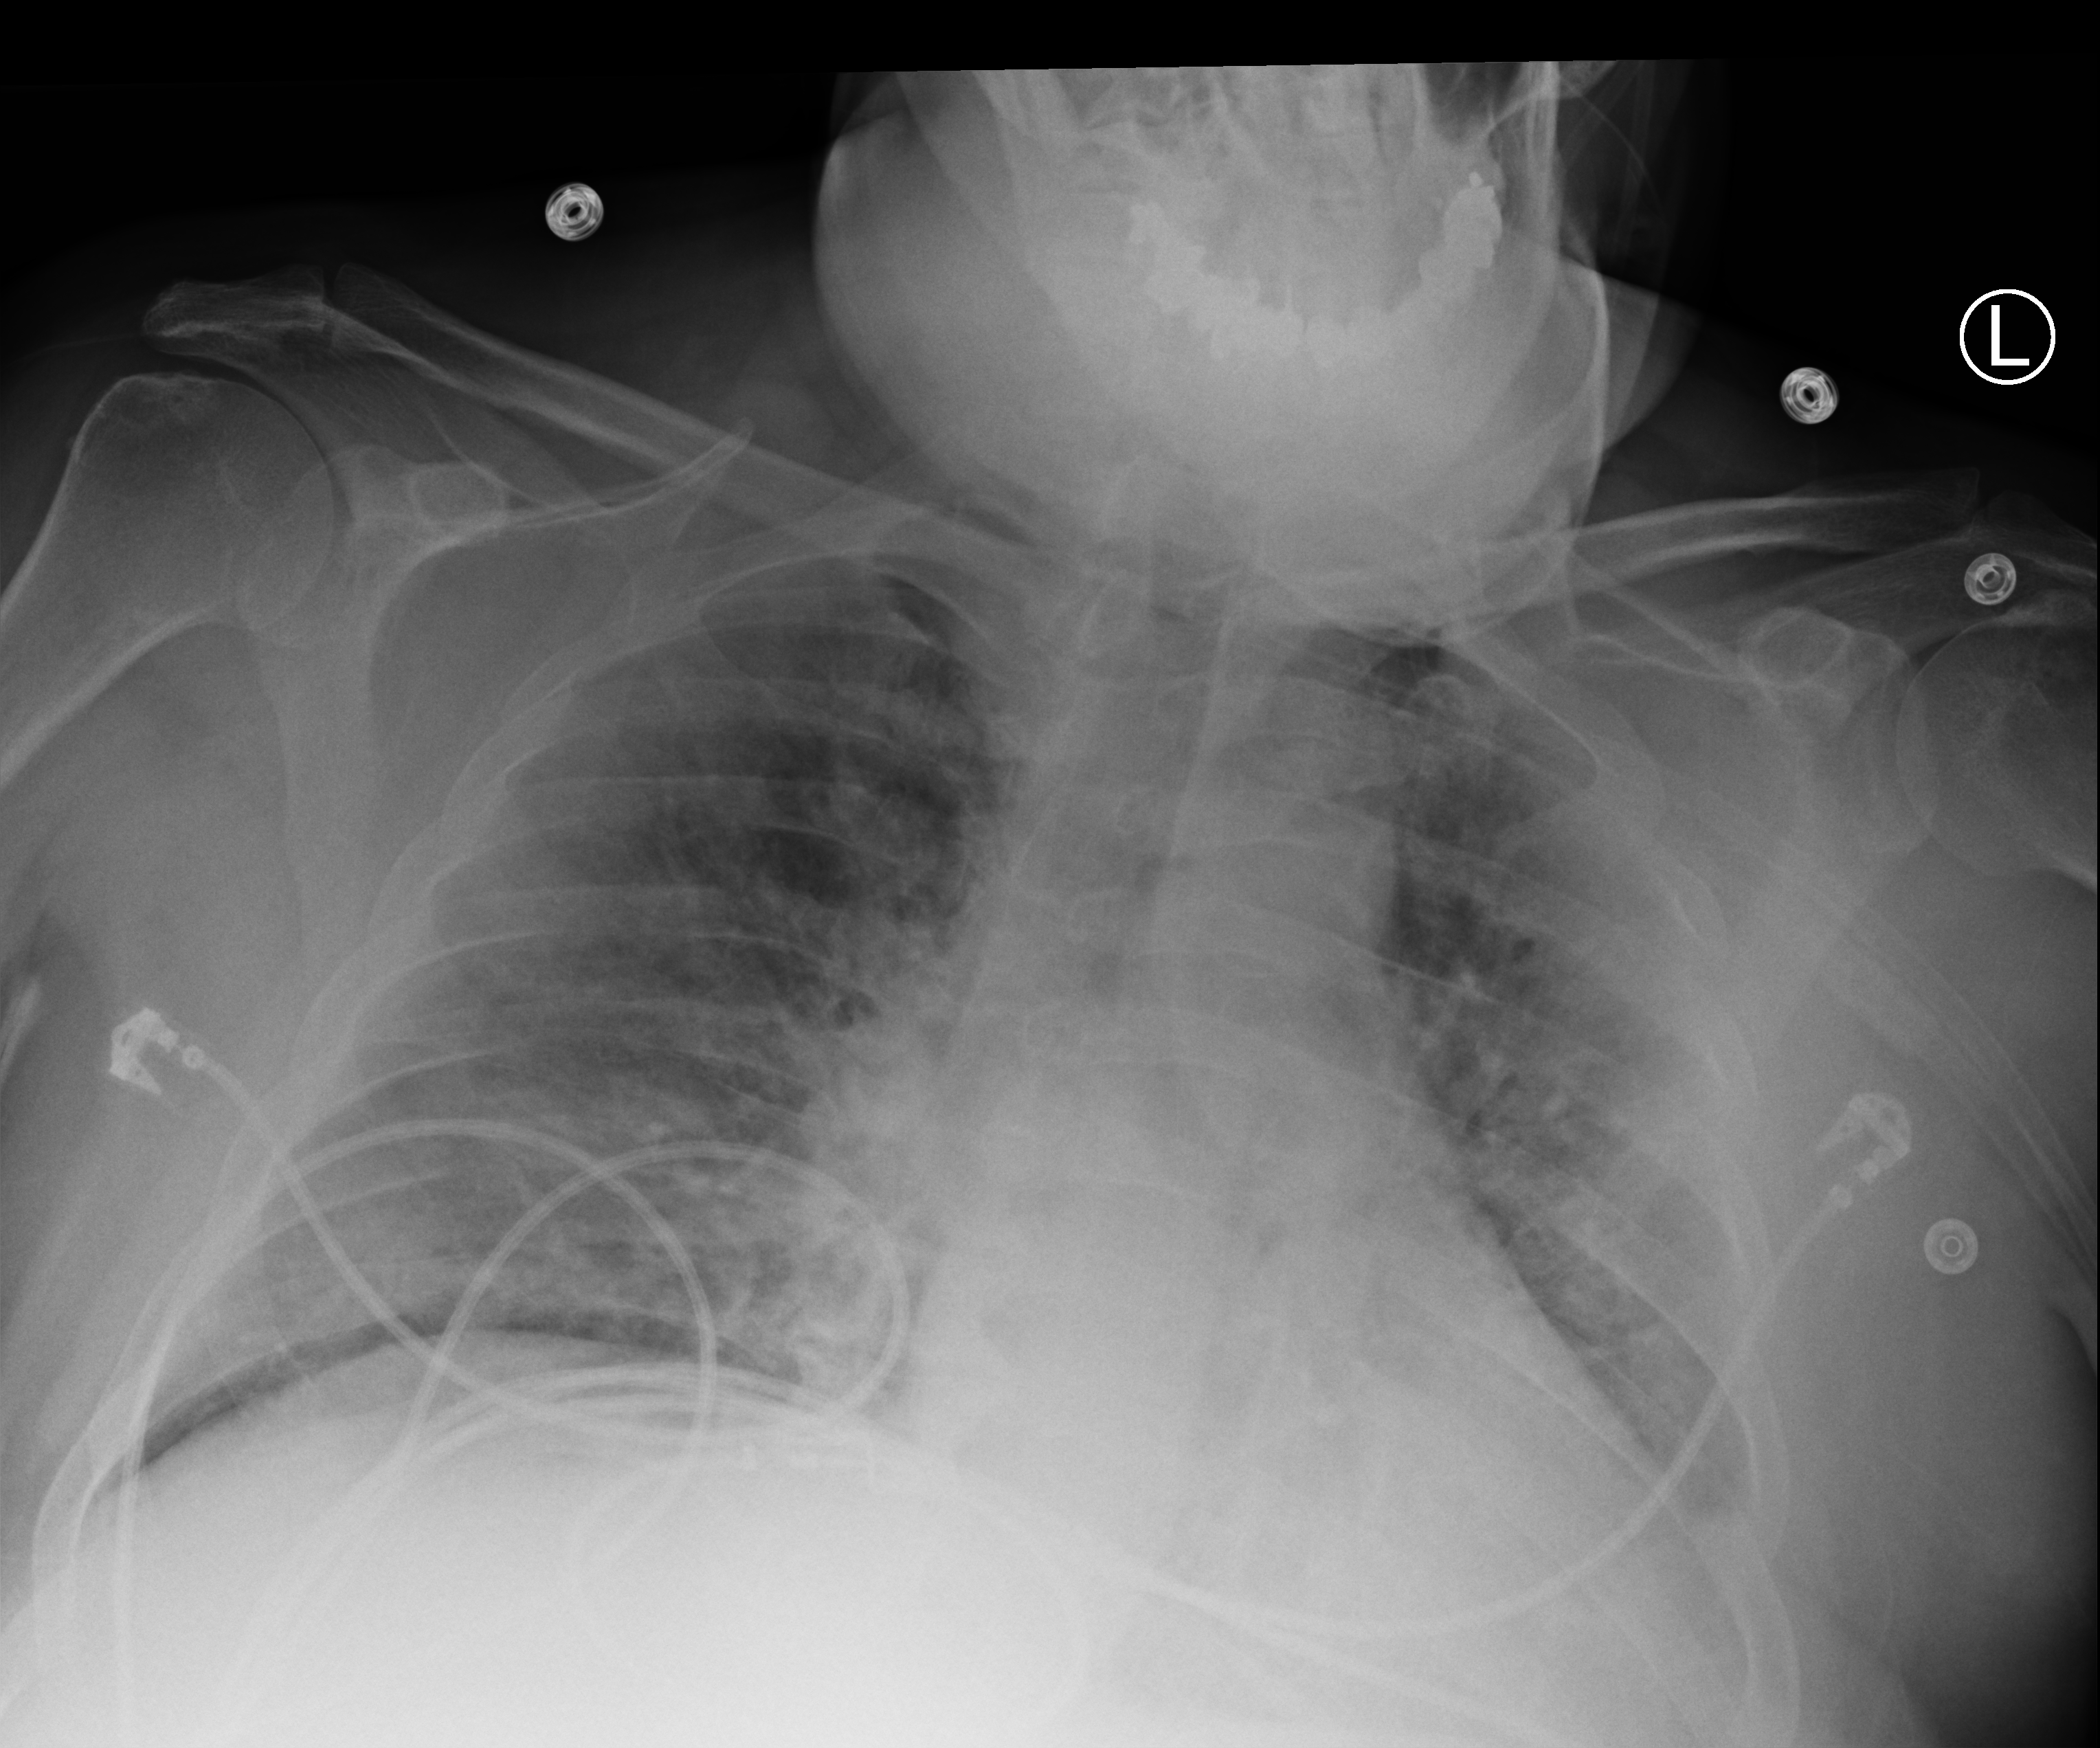
Chest X-ray (portable); anteroposterior (AP) projection. Male patient hospitalised with COVID-19, age 18–59 years.
Hospital-stay facts (about this admission, not read from this image; timing relative to this image not recorded):
- chronic kidney disease (admission record): no
- mechanically ventilated during this hospital stay: no
- diabetes (admission record): yes